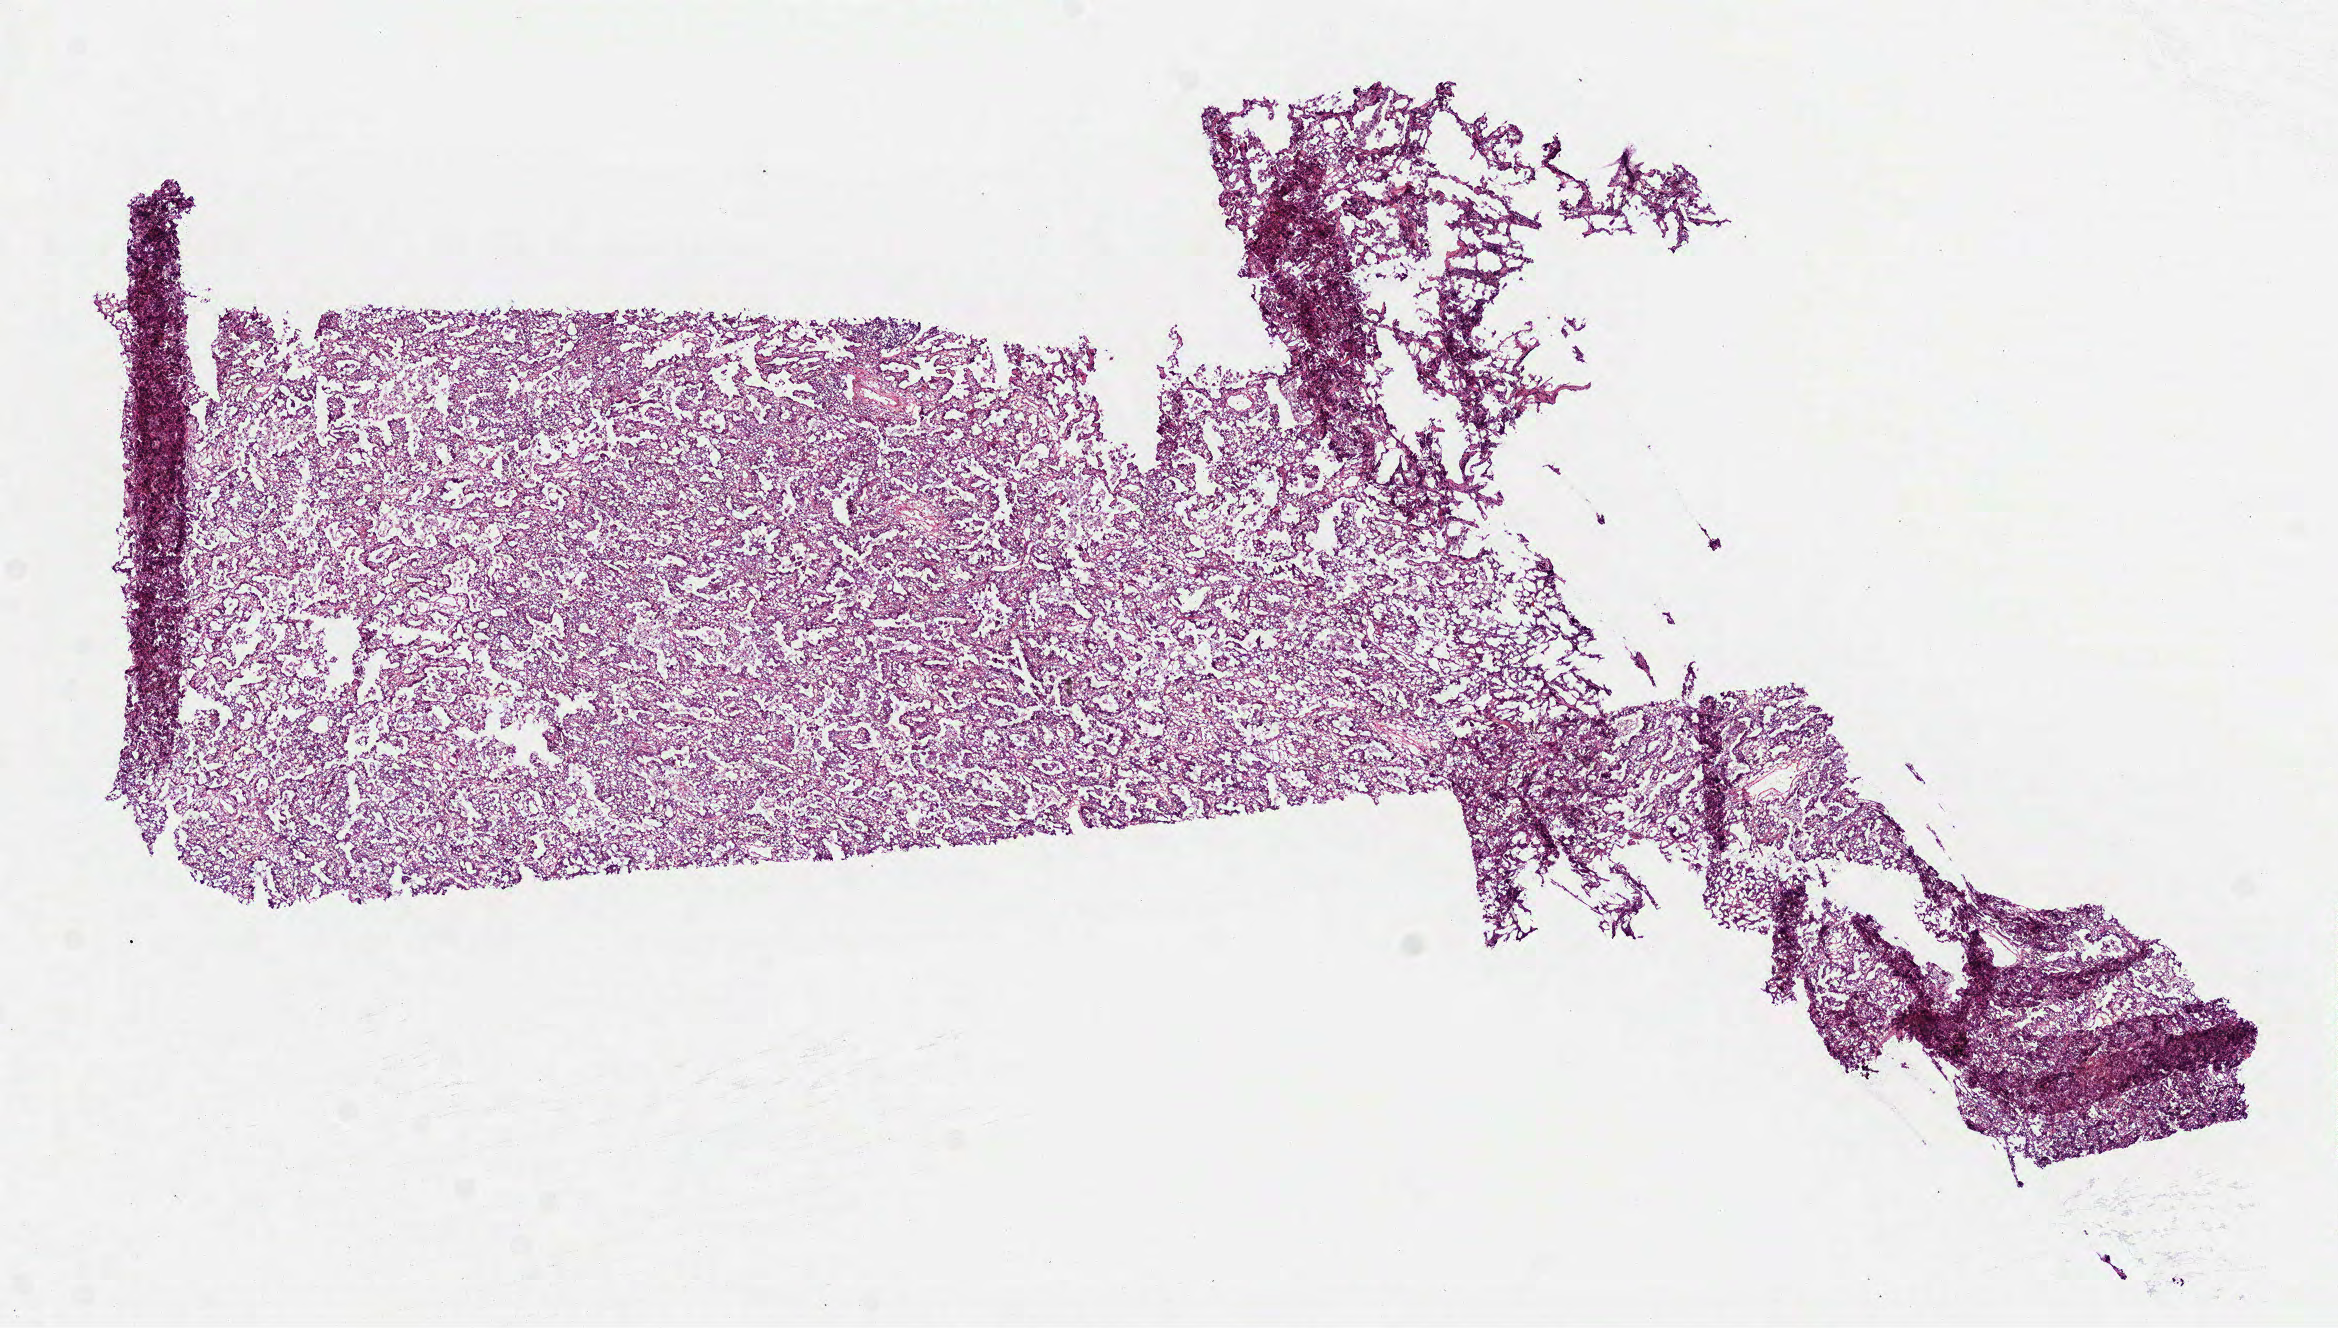
Hematoxylin and eosin (H&E) stained whole-slide image, low-resolution overview of the scanned area, about 9.4 x 5.4 mm; frozen section from the top of the tissue portion; sample: primary tumour, lung. Female patient; age at initial diagnosis 62 years. Pathologist review of this section (percent, as recorded): tumour cells 93%, tumour nuclei 75%, normal cells 0%, stromal cells 5%, necrosis 2%.
• laterality: left
• AJCC pathologic stage: IB
• histologic diagnosis: Bronchiolo-alveolar carcinoma, non-mucinous (upper lobe, lung)